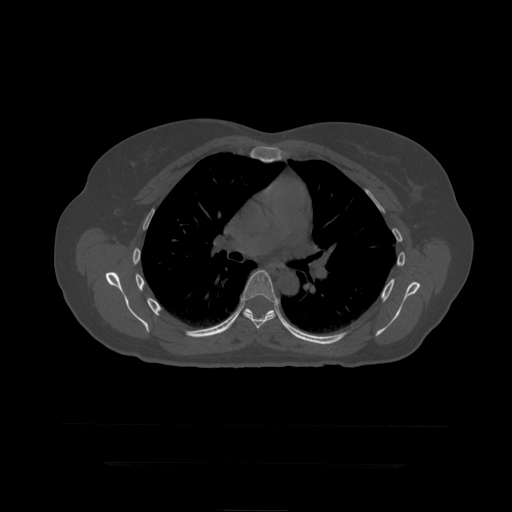
CT including the spine, one axial slice. Position 297 of 399 along the scan axis. Reconstruction kernel STANDARD. 120 kVp. Bone window (W 1800 / L 400 HU). 1.25 mm slice thickness. 512 × 512 image matrix, field of view 450 × 450 mm. Patient age 41 years. Case-level facts recorded for this patient, not image findings: primary cancer: breast.
Annotated regions visible in this slice (semi-automatic segmentation, software-assisted and operator-edited):
- T7 vertebra: box from (x=243, y=270) to (x=277, y=329) px
- T8 vertebra: (x=243, y=308)–(x=275, y=315)